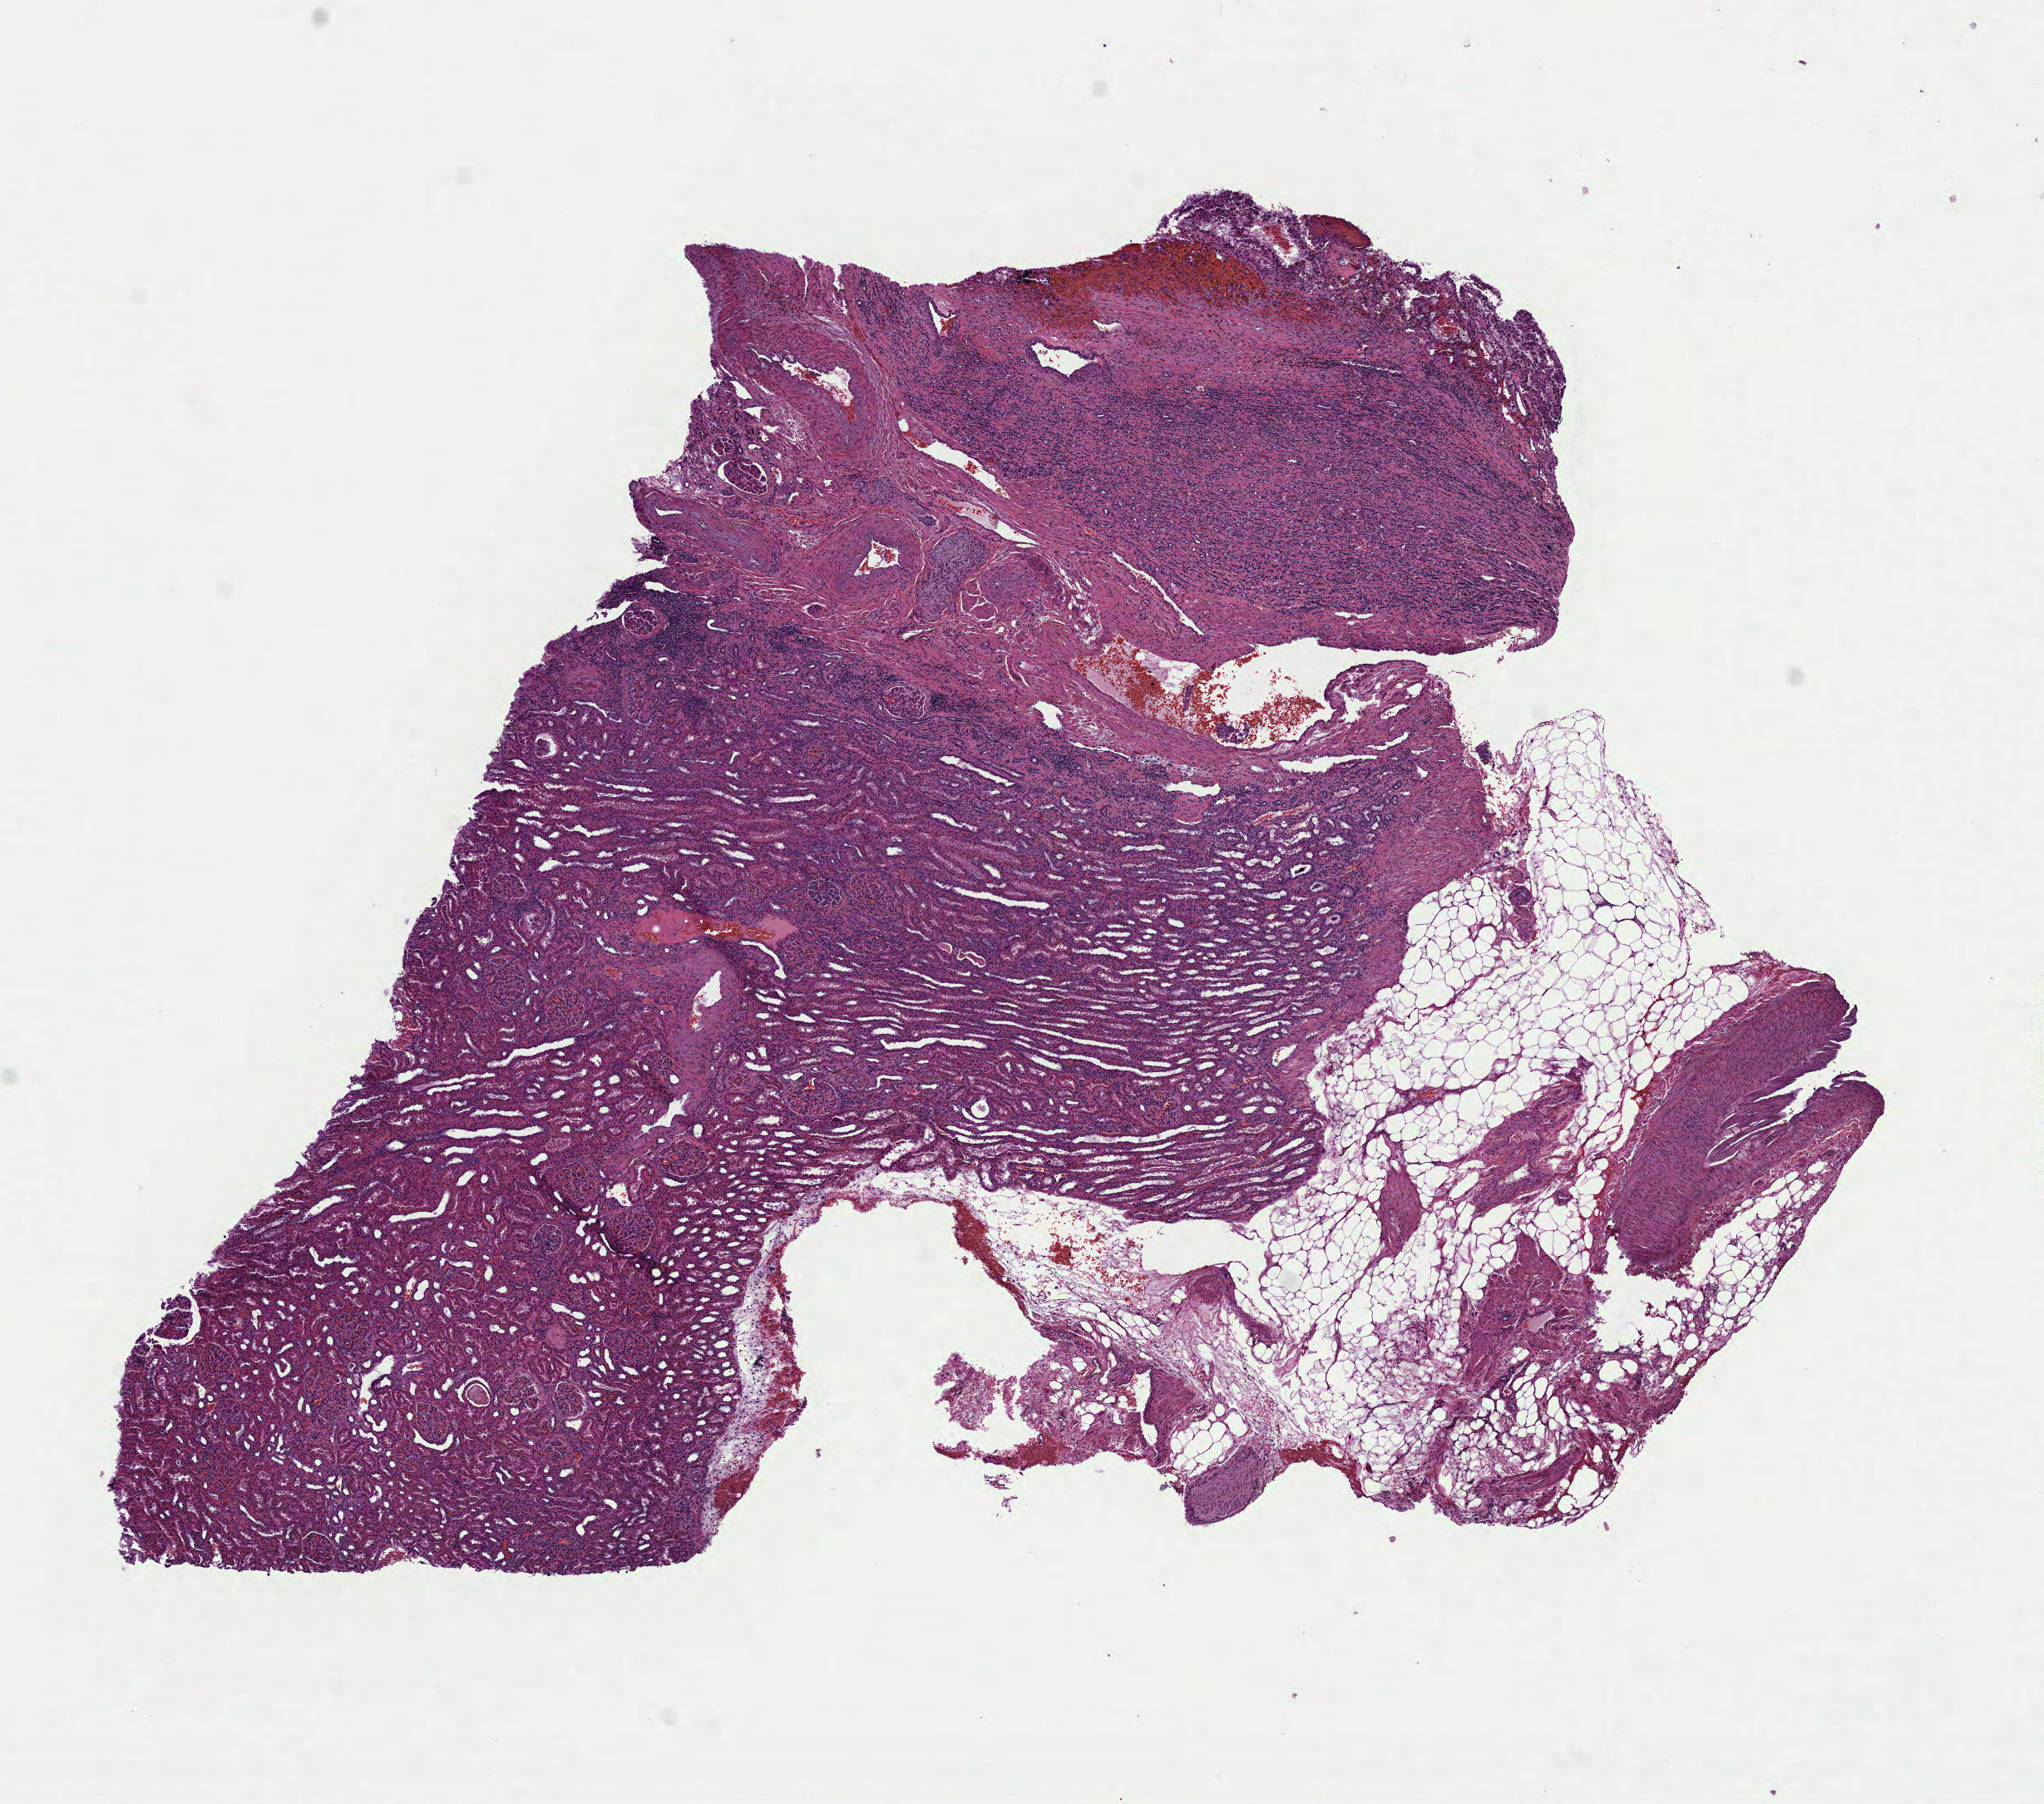
H&E whole-slide image — low-resolution overview of the scanned area, about 9.9 x 8.7 mm; formalin-fixed paraffin-embedded (FFPE) diagnostic section; sample: primary tumour, kidney. Patient: female, age at initial diagnosis 65 years. Histologic grade: G3 (poorly differentiated).
- pathologic diagnosis: Clear cell adenocarcinoma, NOS
- laterality: left
- AJCC pathologic stage: I (7th edition)